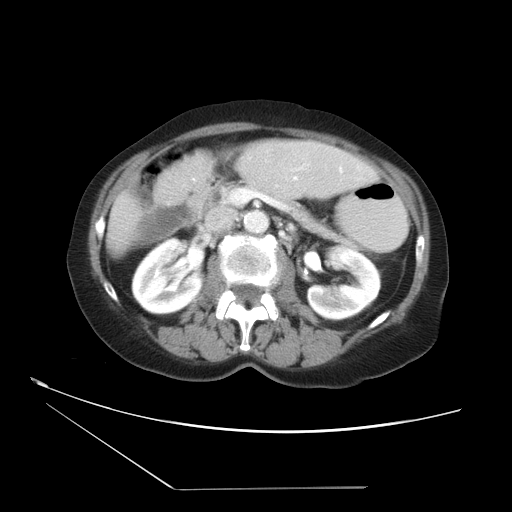
Contrast-enhanced abdominal CT, one axial slice. Position 14 of 36 along the scan axis. Soft-tissue window (W 400 / L 40 HU). 512 × 512 image matrix, field of view 384 × 384 mm. Female patient, age 81 years. Case-level facts recorded for this patient, not image findings: diagnosis: colorectal cancer liver metastases, imaged before liver resection; multiple liver metastases: no; largest metastasis: 1.6 cm; disease in both lobes: no.
Annotated regions visible in this slice (outlined manually by an expert reader):
- liver: bounding box [x1, y1, x2, y2] px = [108, 141, 379, 256]
- planned liver remnant (the part of the liver to remain after resection): [109, 155, 379, 257]
- portal vein (with intrahepatic branches): [234, 190, 243, 201]
- liver metastasis: [273, 146, 289, 160]